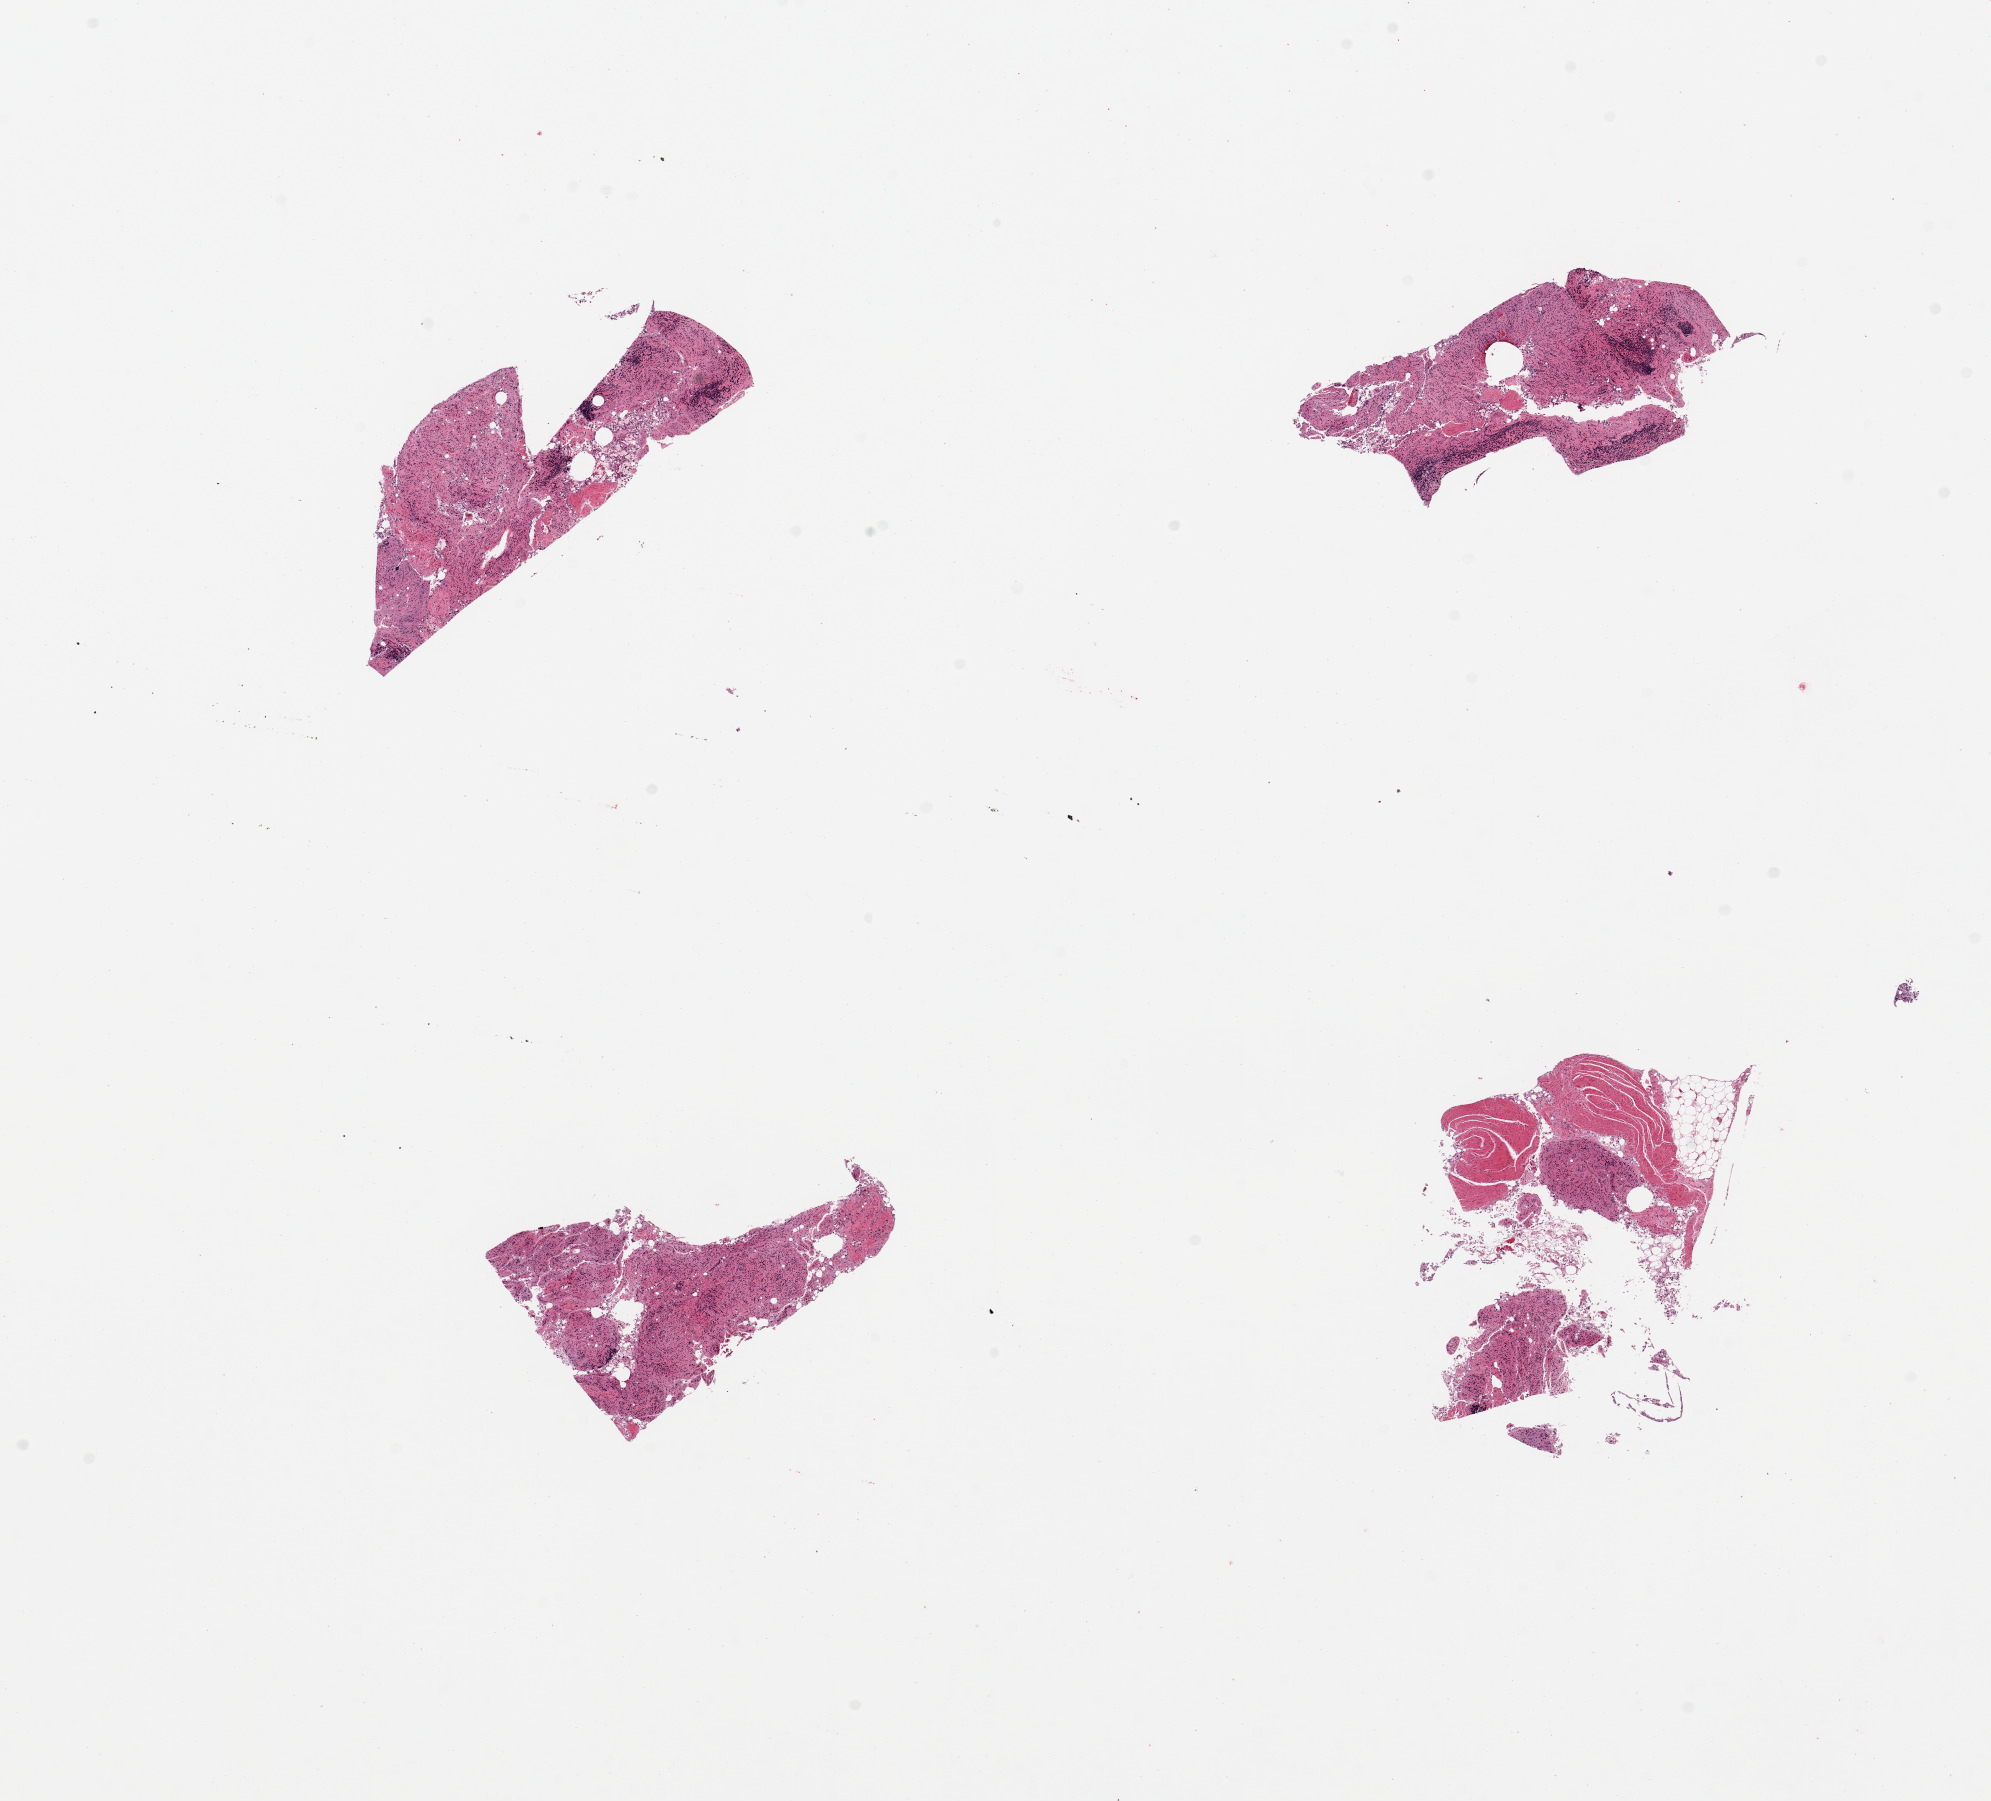
Digitized hematoxylin and eosin (H&E)-stained section — whole scanned area (about 15.8 x 14.2 mm) shown as a low-resolution overview; PAXgene-fixed paraffin-embedded (PFPE) section; target tissue: ileum; donor tissue sample. Donor sex: female.
- pathologist's review note for this sample: 4 pieces; no lymphoid nodules (in autolyzed mucosa)